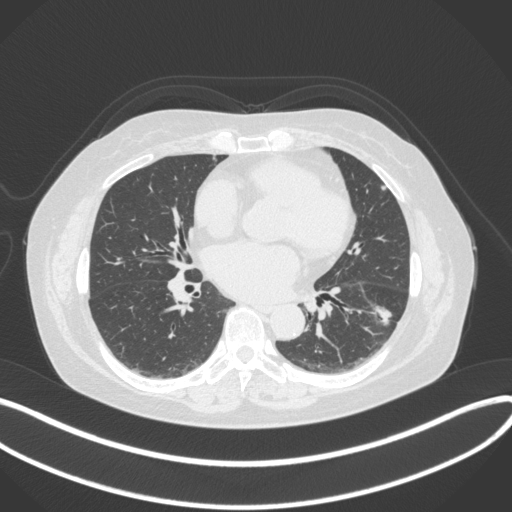
Chest CT, one axial slice. Slice 167 of 373 in the series (ordered by position). 120 kVp. Lung window (W 1500 / L -600 HU). 1 mm slice thickness. 512 × 512 image matrix, field of view 400 × 400 mm. Patient: female, 67 years. Case-level facts recorded for this patient, not image findings: clinical TNM (as recorded): T1c N0 M0.
Outlined on this slice (rectangle marked by the reading radiologist):
- lung tumour (recorded histology: adenocarcinoma): box from (x=364, y=293) to (x=399, y=332) px